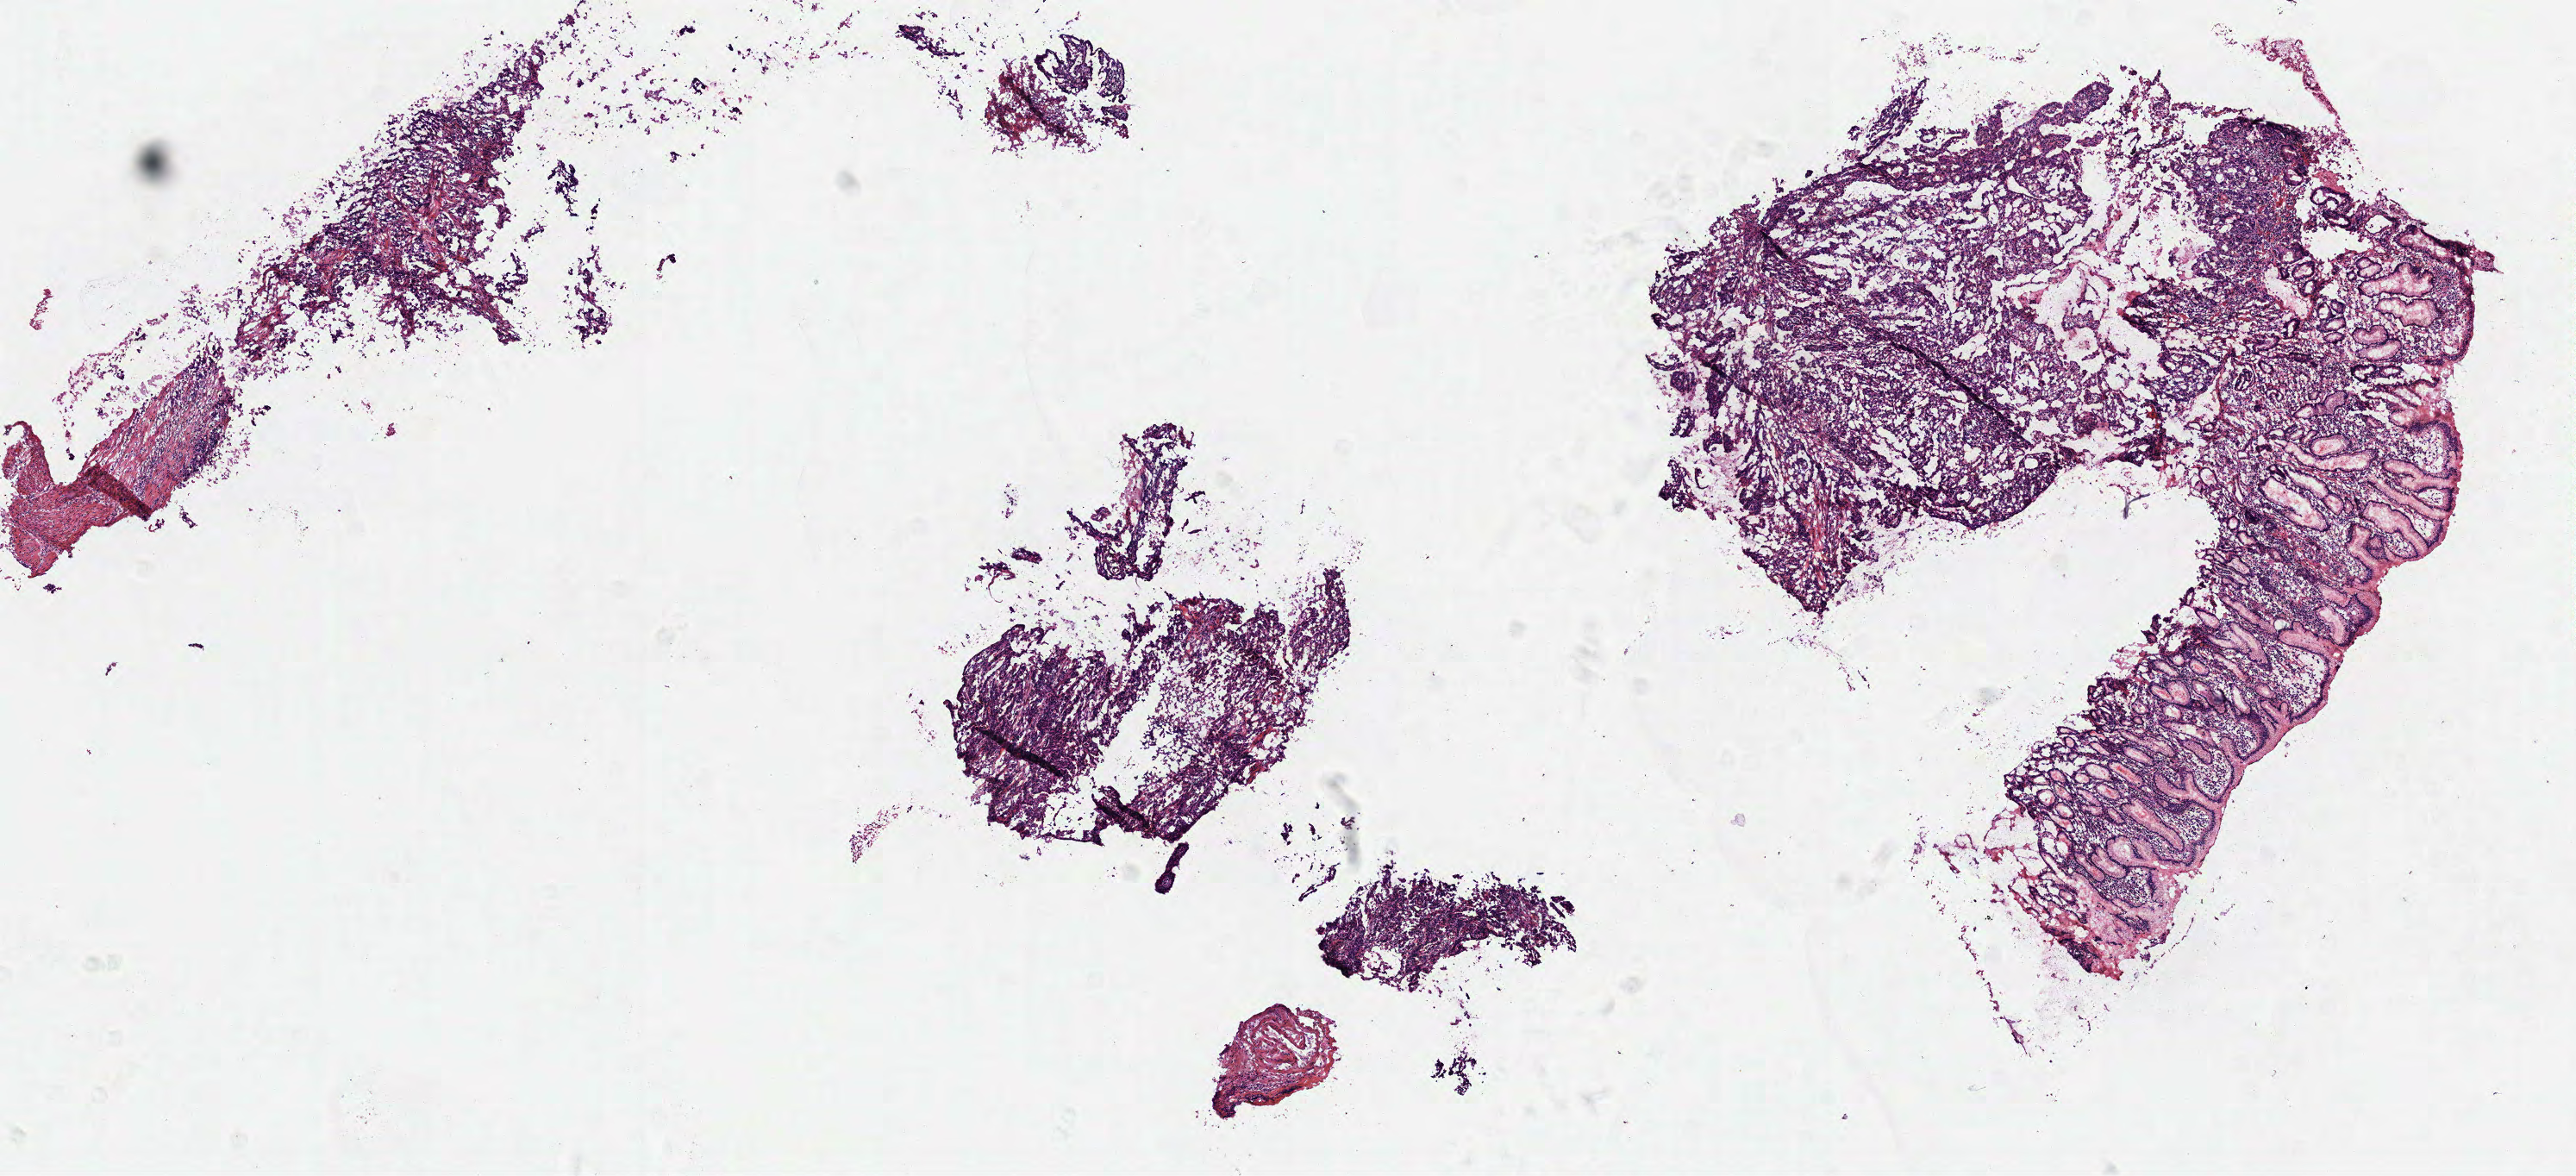
H&E-stained whole-slide image — whole scanned area (about 12.0 x 5.5 mm, acquisition: 40x scan) shown as a low-resolution overview, frozen section, sample: primary tumour, stomach. Patient: male, age at initial diagnosis 74 years. Histologic grade: G3 (poorly differentiated). Composition of this section per pathologist review: tumour cells 60%, tumour nuclei 65%, normal cells 30%, stromal cells 10%, necrosis 0%.
AJCC pathologic stage: II (6th edition). Pathologic diagnosis: Adenocarcinoma, NOS (fundus of stomach).